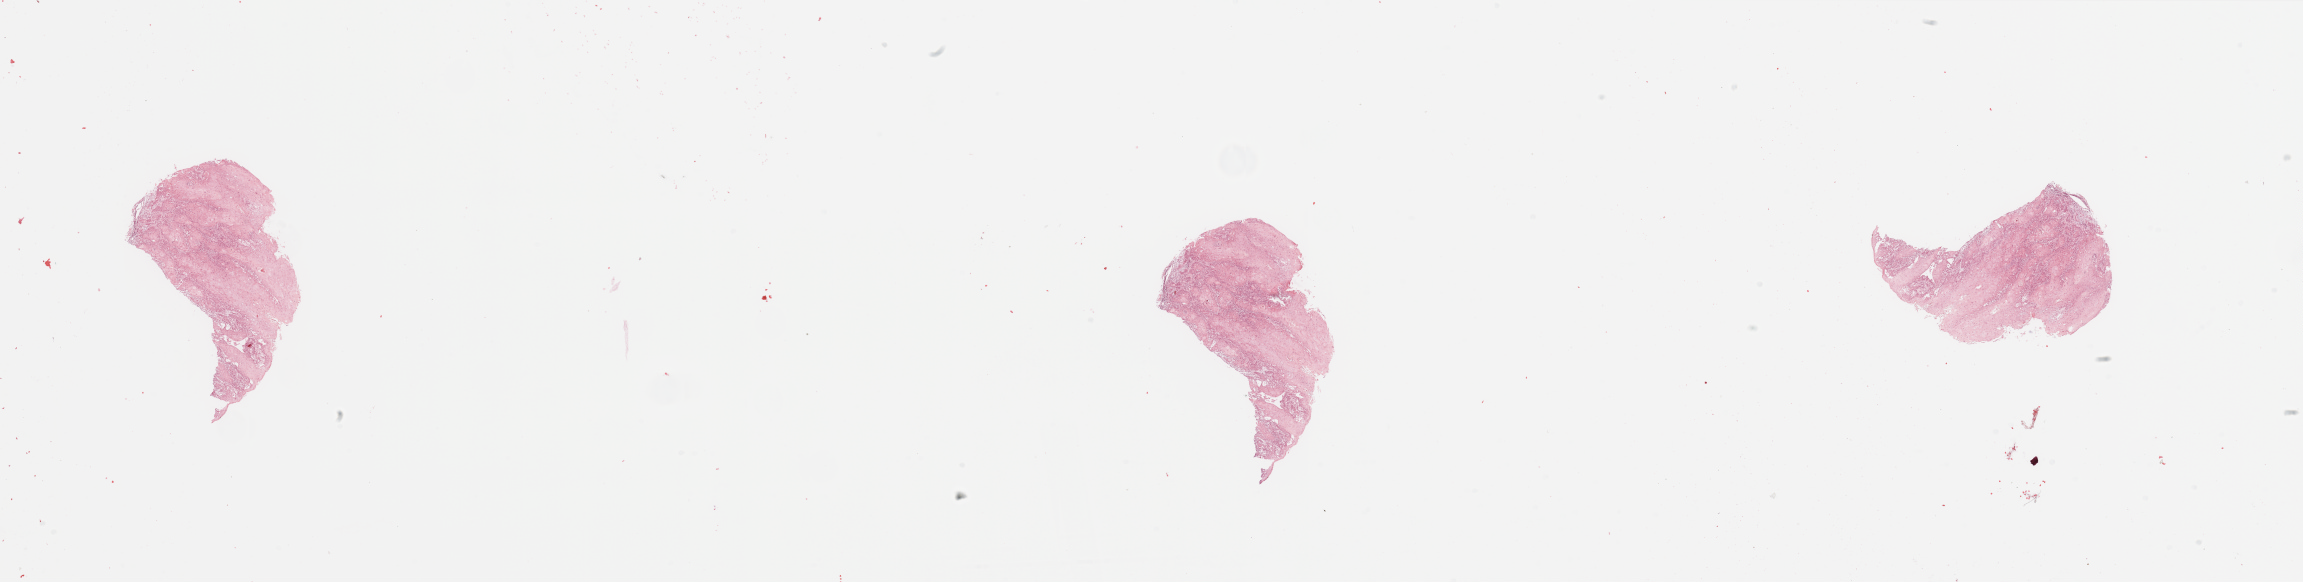
Hematoxylin and eosin (H&E) stained whole-slide image — whole scanned area (about 36.4 x 9.2 mm) shown as a low-resolution overview; tumour tissue sample, sampled site: floor of mouth. Male, 45 y/o. Histologic grade: G1 (well differentiated). Composition of this section per pathologist review: tumour nuclei 80%, necrosis 10%.
• AJCC pathologic stage: III
• diagnosis: Squamous cell carcinoma, NOS (floor of mouth, NOS)
• primary tumour site (as recorded): oral cavity